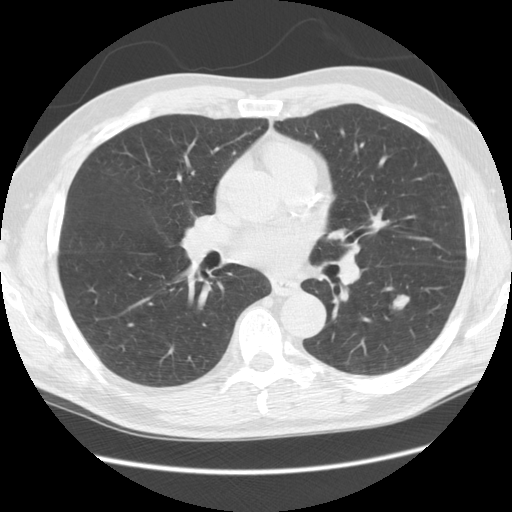
Low-dose screening chest CT, one axial slice. Position 55 of 111 along the scan axis. Reconstruction kernel STANDARD. 120 kVp. Lung window (W 1500 / L -600 HU). 2.5 mm slice thickness. 512 × 512 image matrix.
Structures marked on this image (manually delineated by an expert):
- lesion 1 (tumor, lower lobe of left lung): bounding box <392,294,409,311> (left, top, right, bottom; pixels)